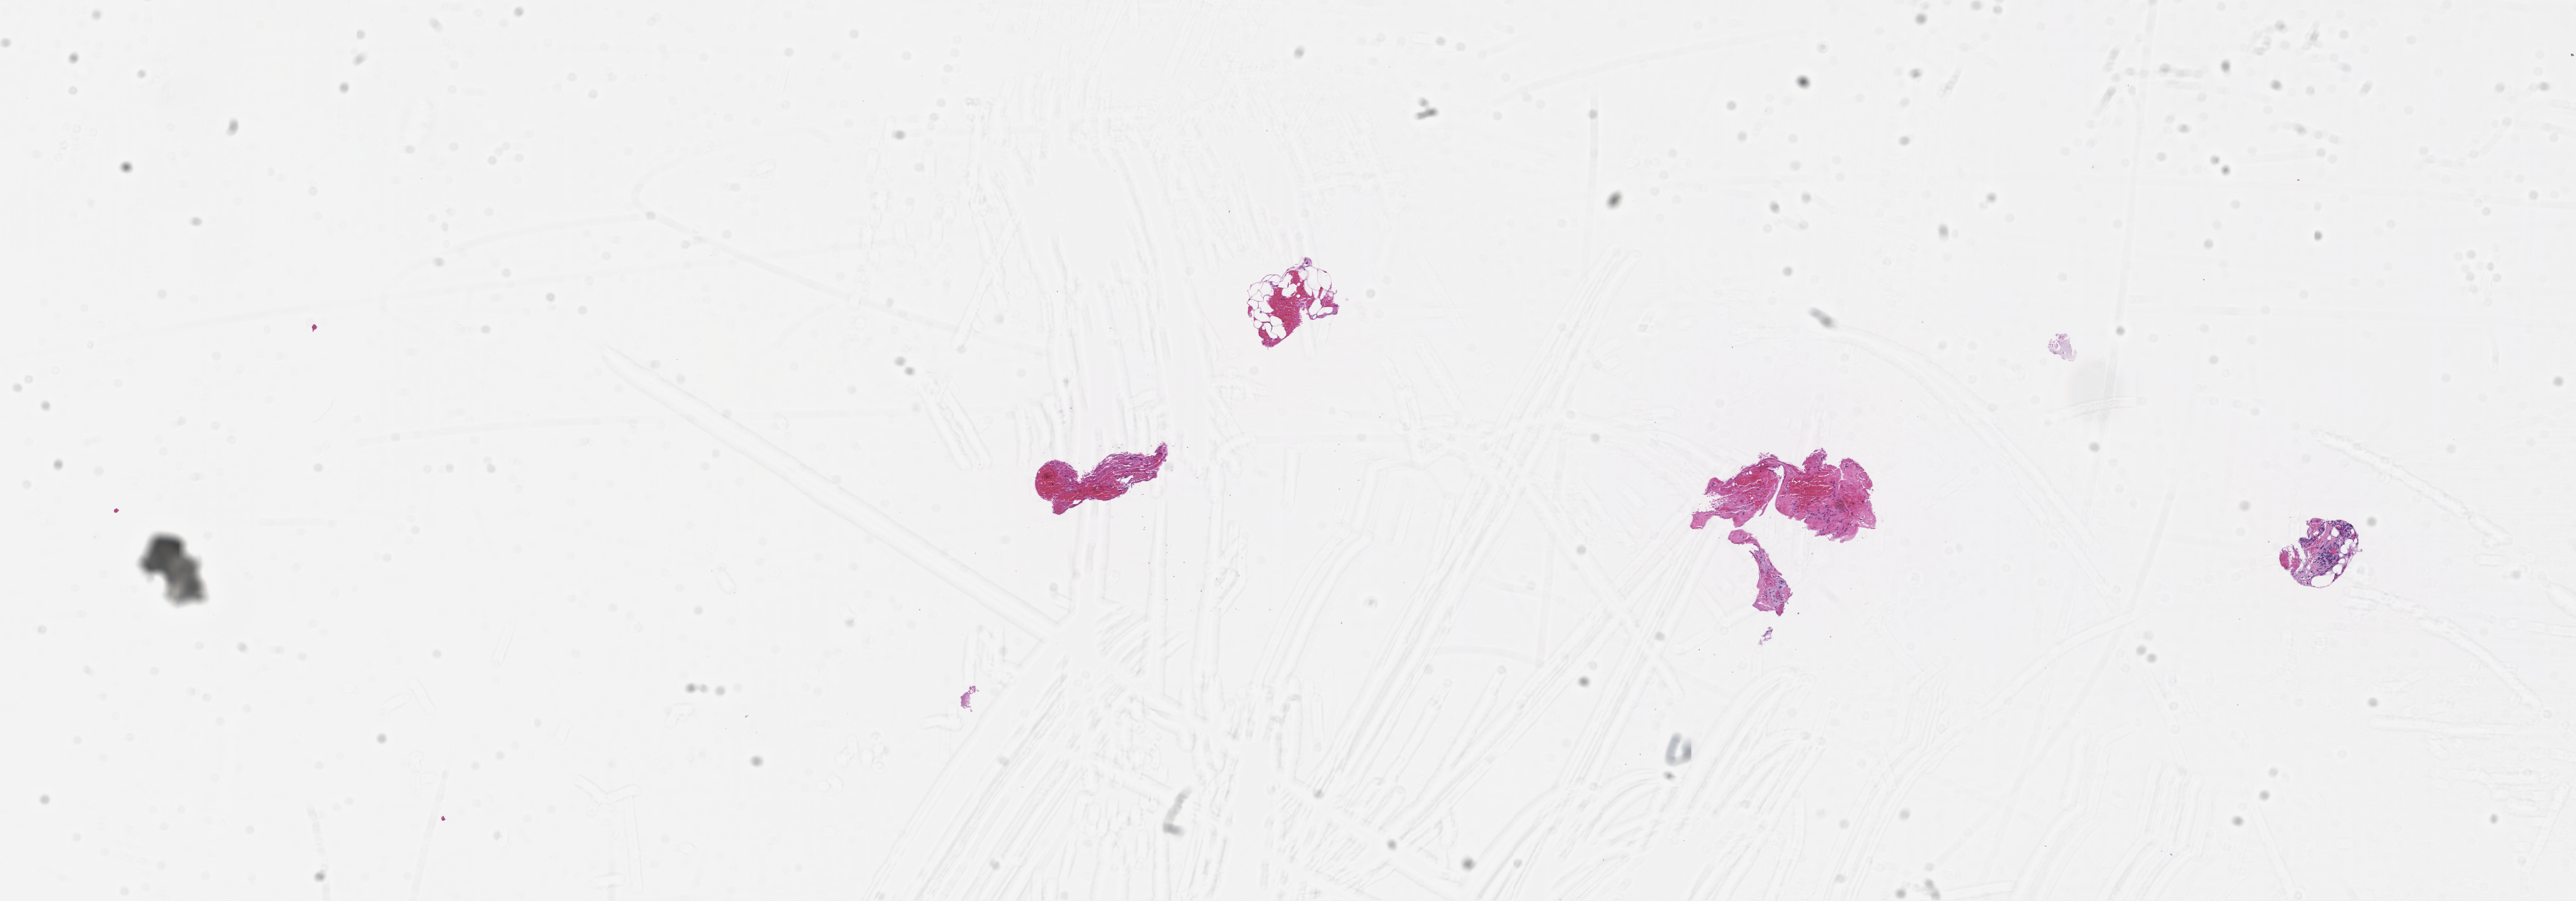
Hematoxylin and eosin (H&E) whole-slide image — shown as a low-resolution overview of the whole scanned area (about 14.6 x 5.1 mm). FFPE section. Collected at baseline (before treatment). Patient: female.
- this section: metastatic tumor tissue
- primary diagnosis of the patient: Colorectal Carcinoma